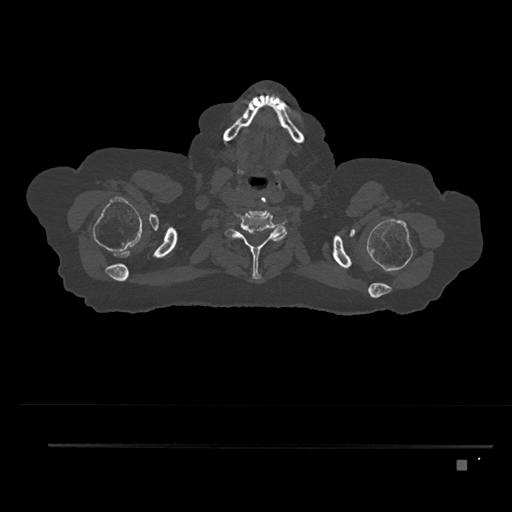
CT including the spine, one axial slice; slice 735 of 797 in the series (ordered by position); 120 kVp; bone window (W 1800 / L 400 HU); 0.5 mm slice thickness; 512 × 512 image matrix, field of view 437 × 437 mm. Patient: female, 76 years. From the clinical record (not read from this slice): primary cancer: lung; vertebrae with lytic lesions (as recorded): T11, L3.
Annotated regions visible in this slice (semi-automatic segmentation, software-assisted and operator-edited):
- T1 vertebra: bounding box (x1, y1, x2, y2) in pixels: (246, 244, 252, 252)